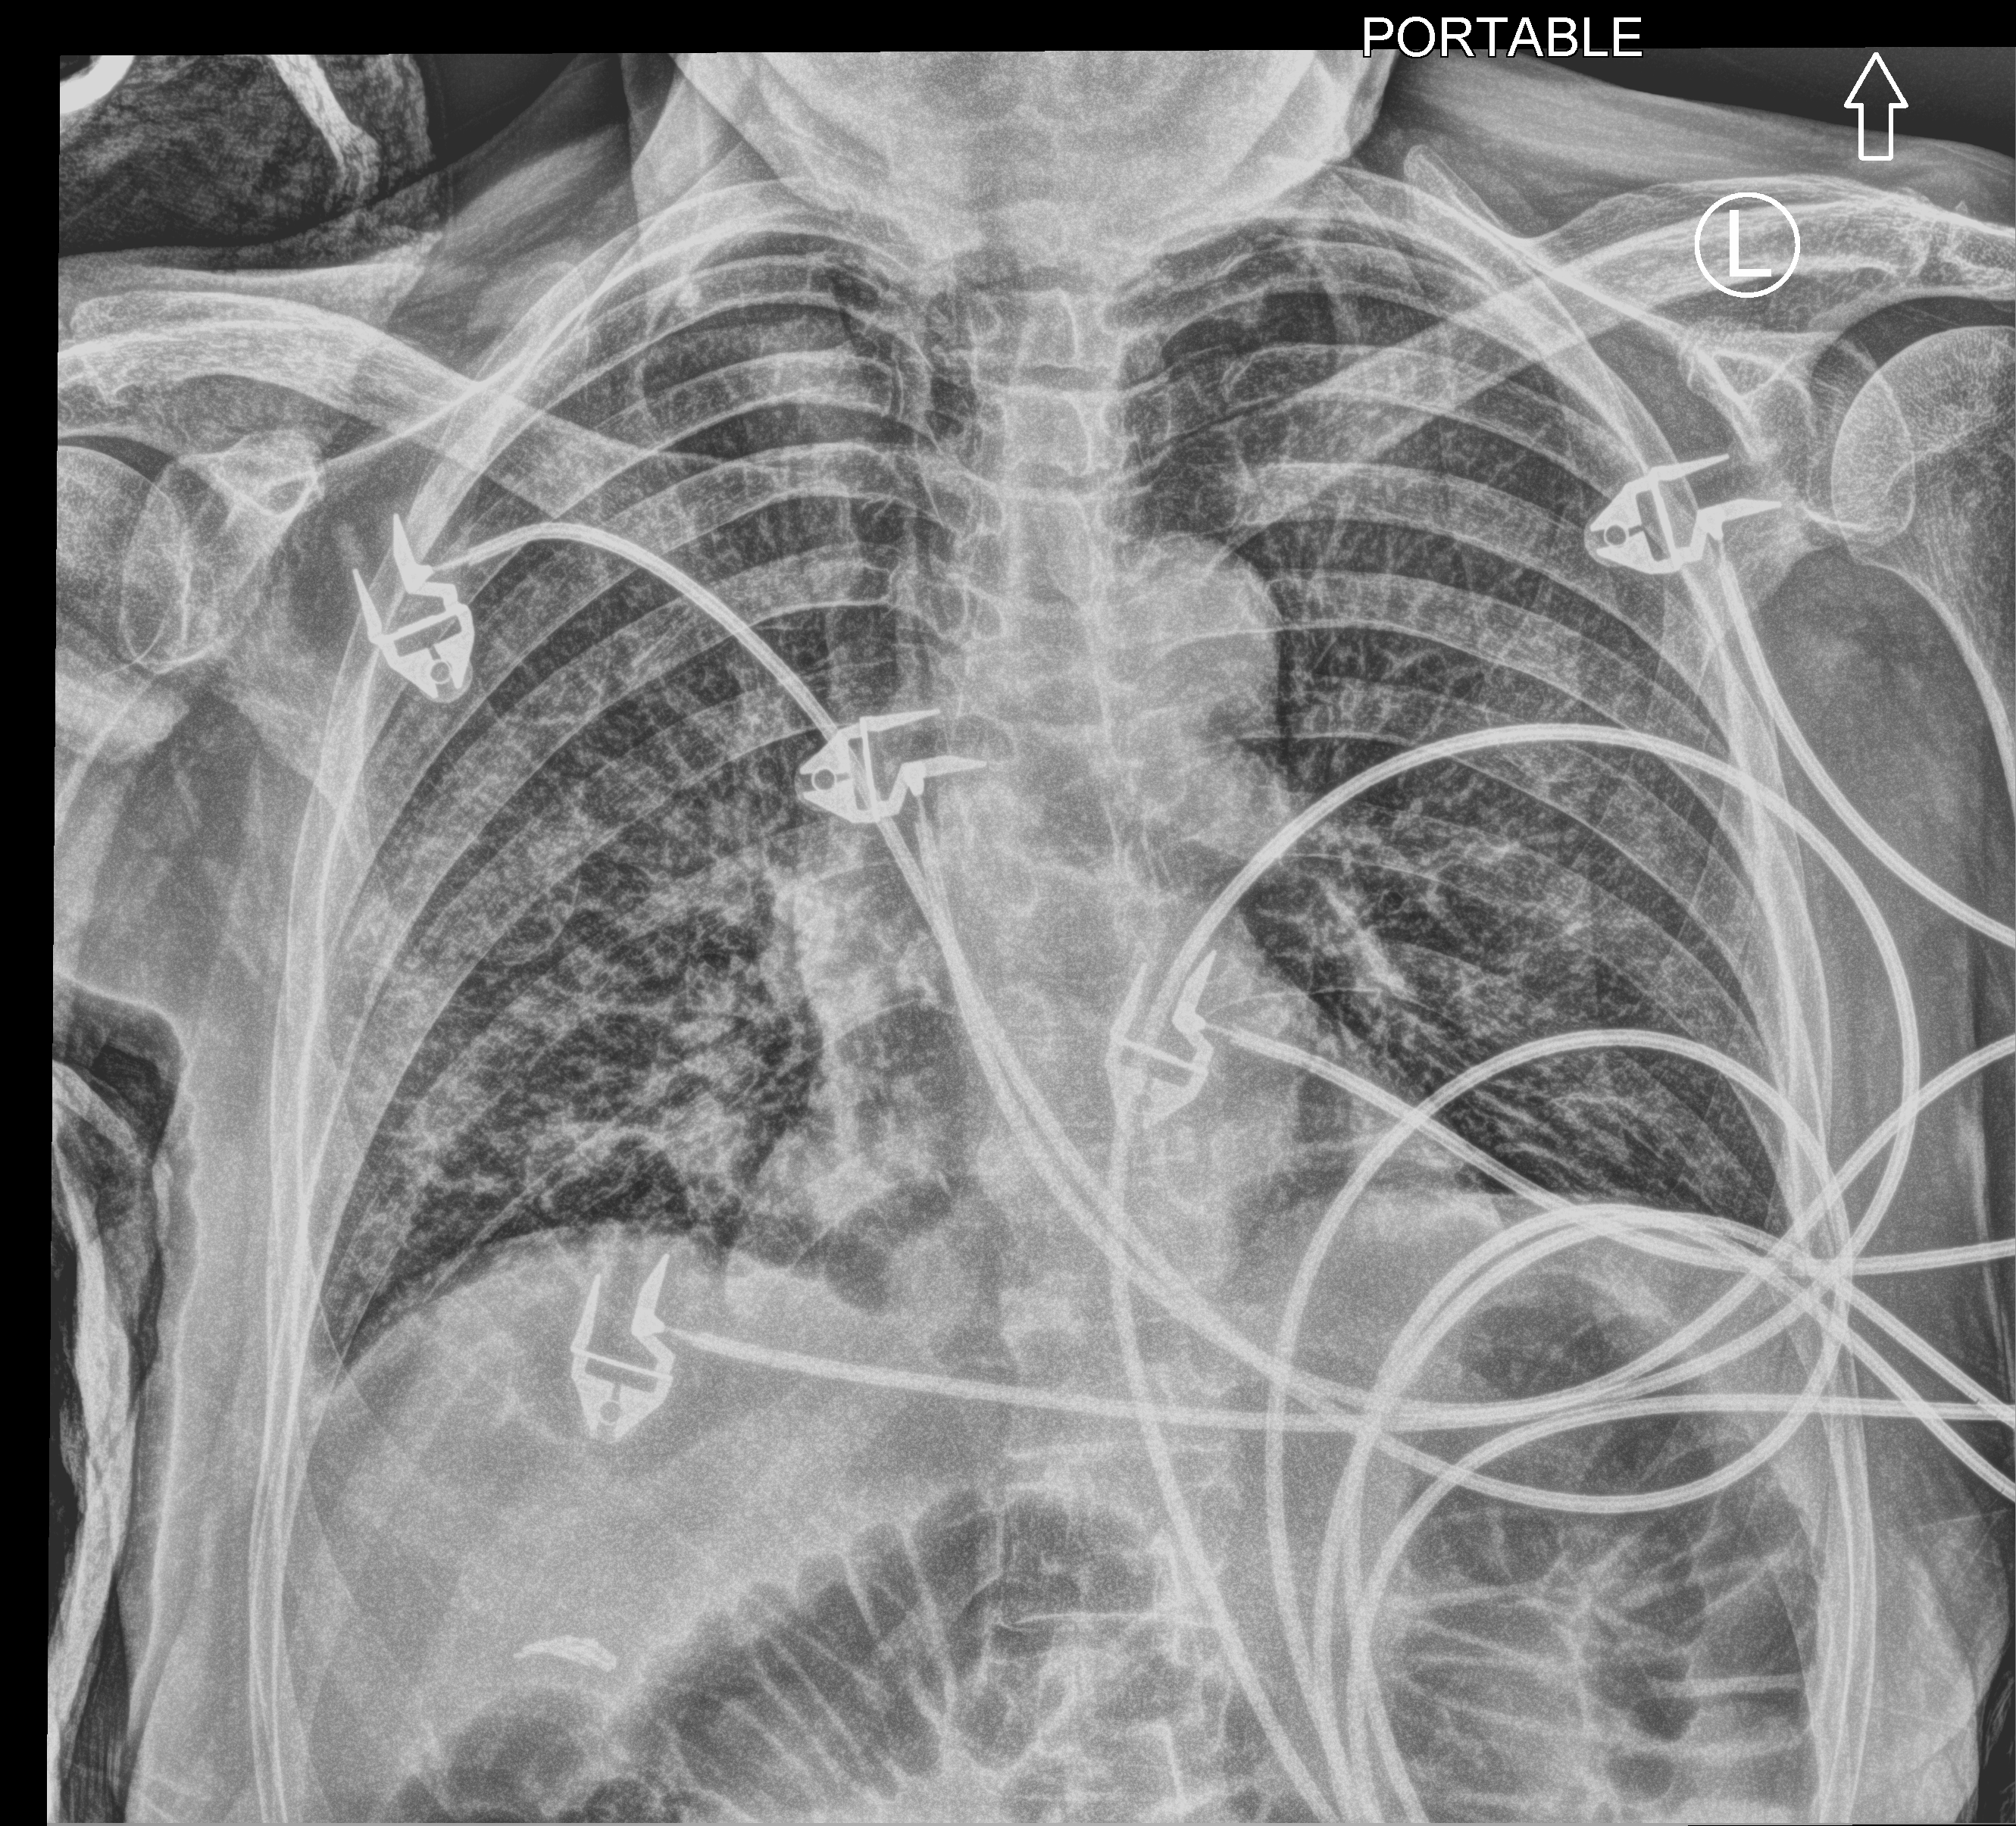
Portable chest radiograph; anteroposterior (AP) projection. Patient hospitalised with COVID-19; female, aged 75–90 years.
From the hospital-stay record, not from the radiograph (when in the stay this image was taken is not recorded):
- length of hospital stay: 9 days
- admitted to intensive care during this hospital stay: no
- mechanically ventilated during this hospital stay: no